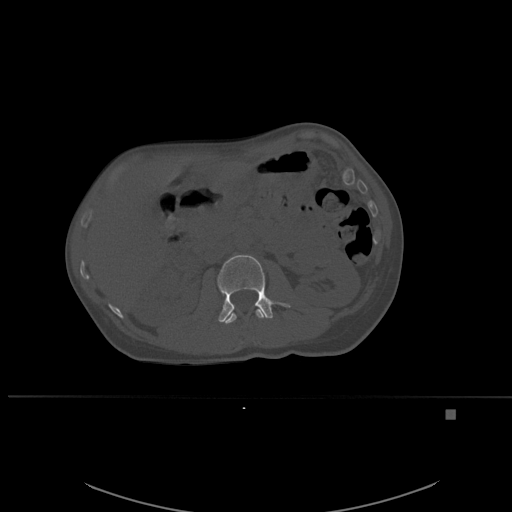
CT including the spine, one axial slice. Position 243 of 537 along the scan axis. Bone window (W 1800 / L 400 HU). 512 × 512 image matrix, field of view 440 × 440 mm. Patient: female, 45 years. Case-level facts recorded for this patient, not image findings: primary cancer: lung.
Annotated regions visible in this slice (semi-automatic segmentation, software-assisted and operator-edited):
- L1 vertebra: bounding box <224,308,264,324> (left, top, right, bottom; pixels)
- L2 vertebra: <217,255,290,322>